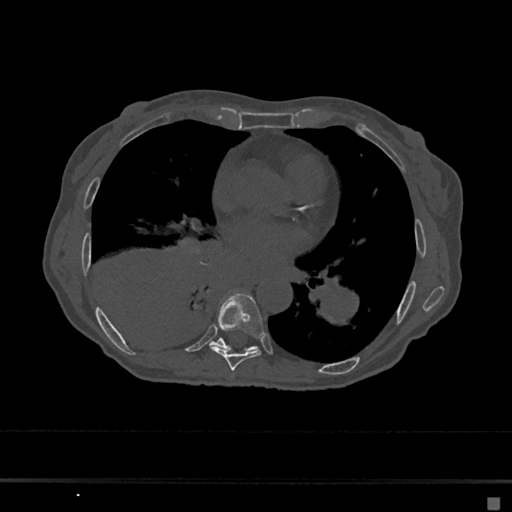
CT including the spine, one axial slice; reconstruction kernel Br40s/3; bone window (W 1800 / L 400 HU); 0.5 mm slice thickness; 512 × 512 image matrix, field of view 360 × 360 mm. Patient: female, 68 years. From the clinical record (not read from this slice): primary cancer: renal.
Structures marked on this image (semi-automatic segmentation, software-assisted and operator-edited):
- T7 vertebra: bounding box <210,292,264,371> (left, top, right, bottom; pixels)
- T8 vertebra: <212,339,256,351>